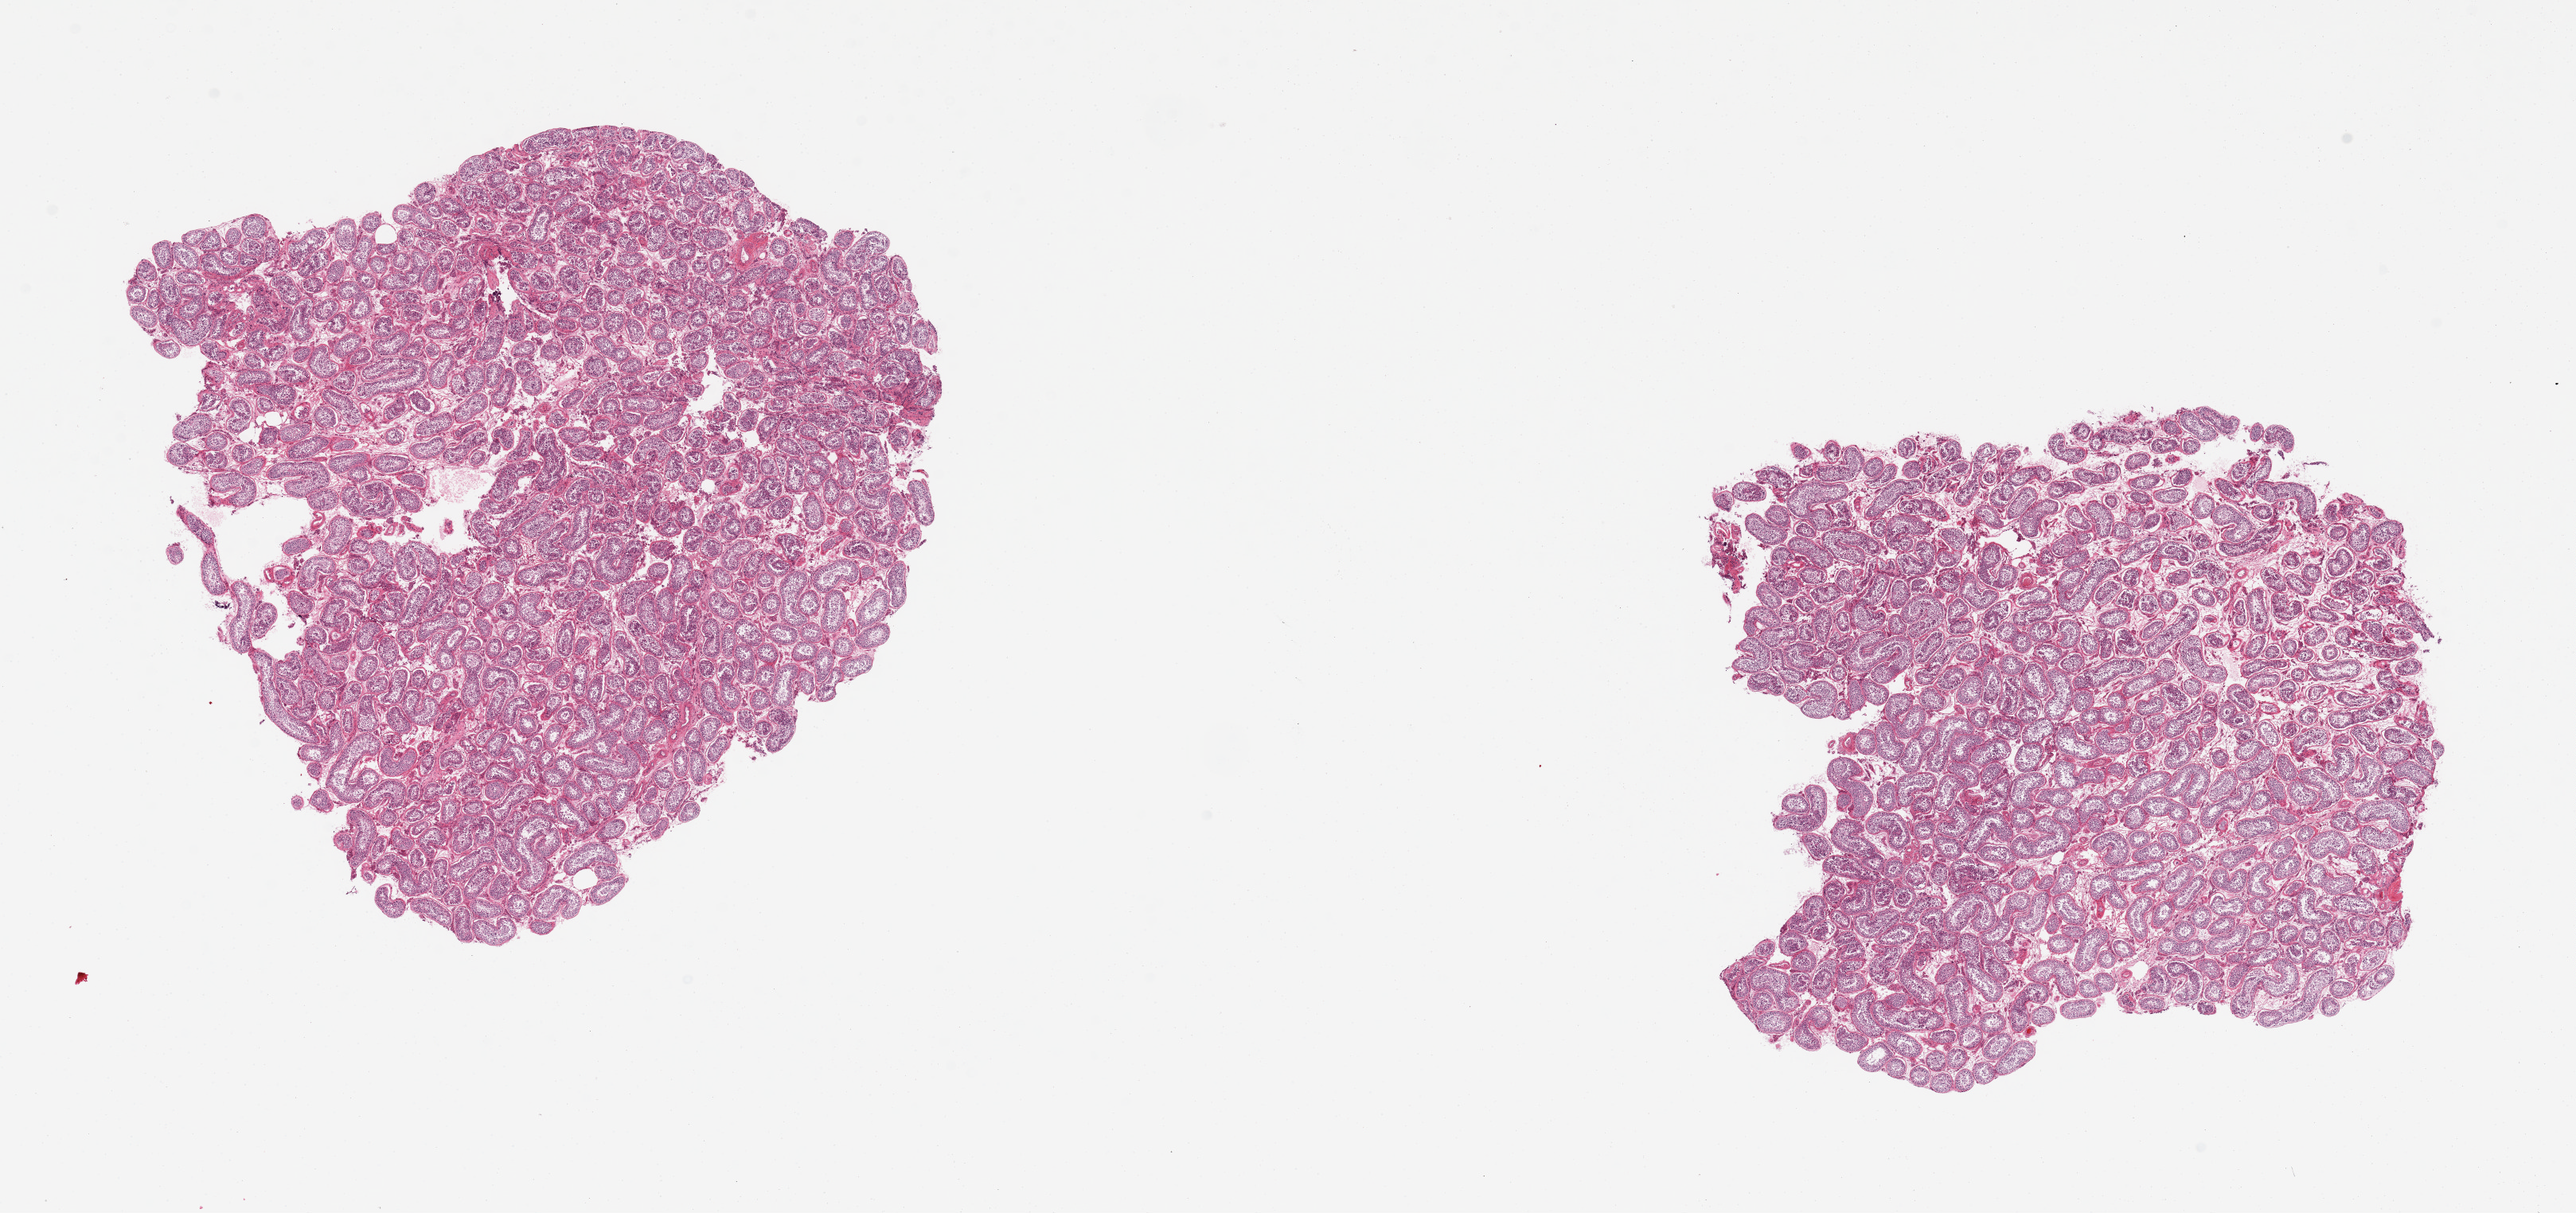
Digitized hematoxylin and eosin (H&E)-stained section, low-resolution overview of the scanned area, about 25.6 x 12.1 mm. PAXgene-fixed, paraffin-embedded tissue. Section of testis (target tissue). Donor tissue sample. Male donor.
Reviewer comment on this tissue sample: 2 pieces. Active spermatogenesis.